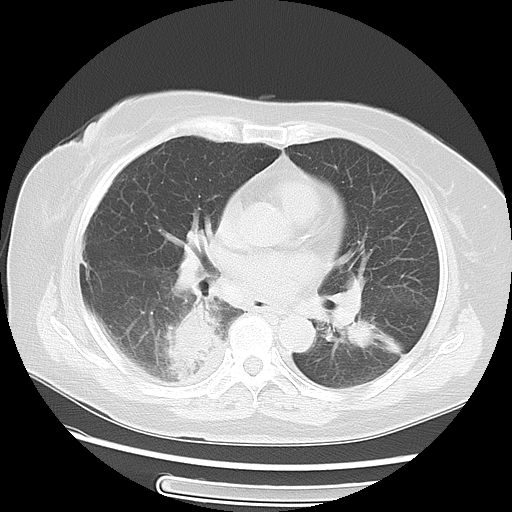
Chest CT, one axial slice. Position 31 of 57 along the scan axis. Reconstruction kernel LUNG. 120 kVp. Lung window (W 1500 / L -600 HU). 5 mm slice thickness. 512 × 512 image matrix, field of view 350 × 350 mm. Patient: female, 69 years. From the clinical record (not read from this slice): clinical TNM (as recorded): T2 N1 M1a.
Annotated regions visible in this slice (bounding box drawn by a radiologist):
- lung tumour (recorded histology: adenocarcinoma): box from (x=160, y=298) to (x=224, y=388) px